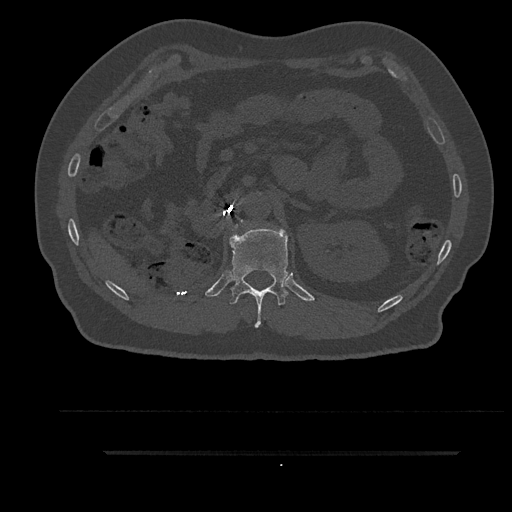
CT including the spine, one axial slice. Slice 236 of 797 in the series (ordered by position). Reconstruction kernel Br40s/3. 120 kVp. Bone window (W 1800 / L 400 HU). 512 × 512 image matrix, field of view 432 × 432 mm. Patient: male, 63 years. Case-level facts recorded for this patient, not image findings: primary cancer: renal.
Structures marked on this image (semi-automatic segmentation, software-assisted and operator-edited):
- L1 vertebra: bounding box <235,221,242,228> (left, top, right, bottom; pixels)
- T12 vertebra: <230,229,288,328>